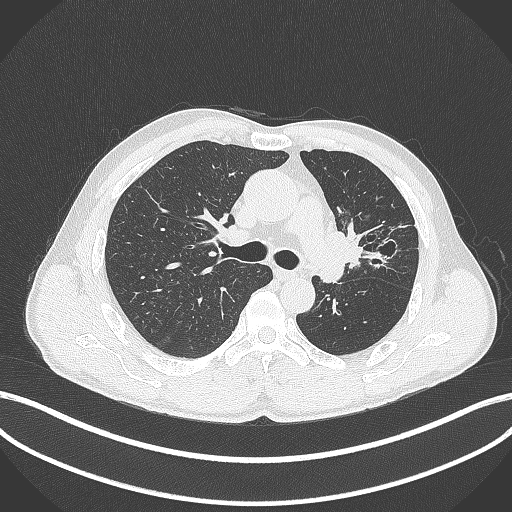
Chest CT, one axial slice; slice 268 of 429 in the series (ordered by position); 120 kVp; lung window (W 1500 / L -600 HU); 1 mm slice thickness; 512 × 512 image matrix, field of view 400 × 400 mm. Patient: male, 57 years. Case-level facts recorded for this patient, not image findings: clinical TNM (as recorded): T2b N0 M0.
Annotated regions visible in this slice (bounding box drawn by a radiologist):
- lung tumour (recorded histology: squamous cell carcinoma): bounding box <319,225,369,271> (left, top, right, bottom; pixels)